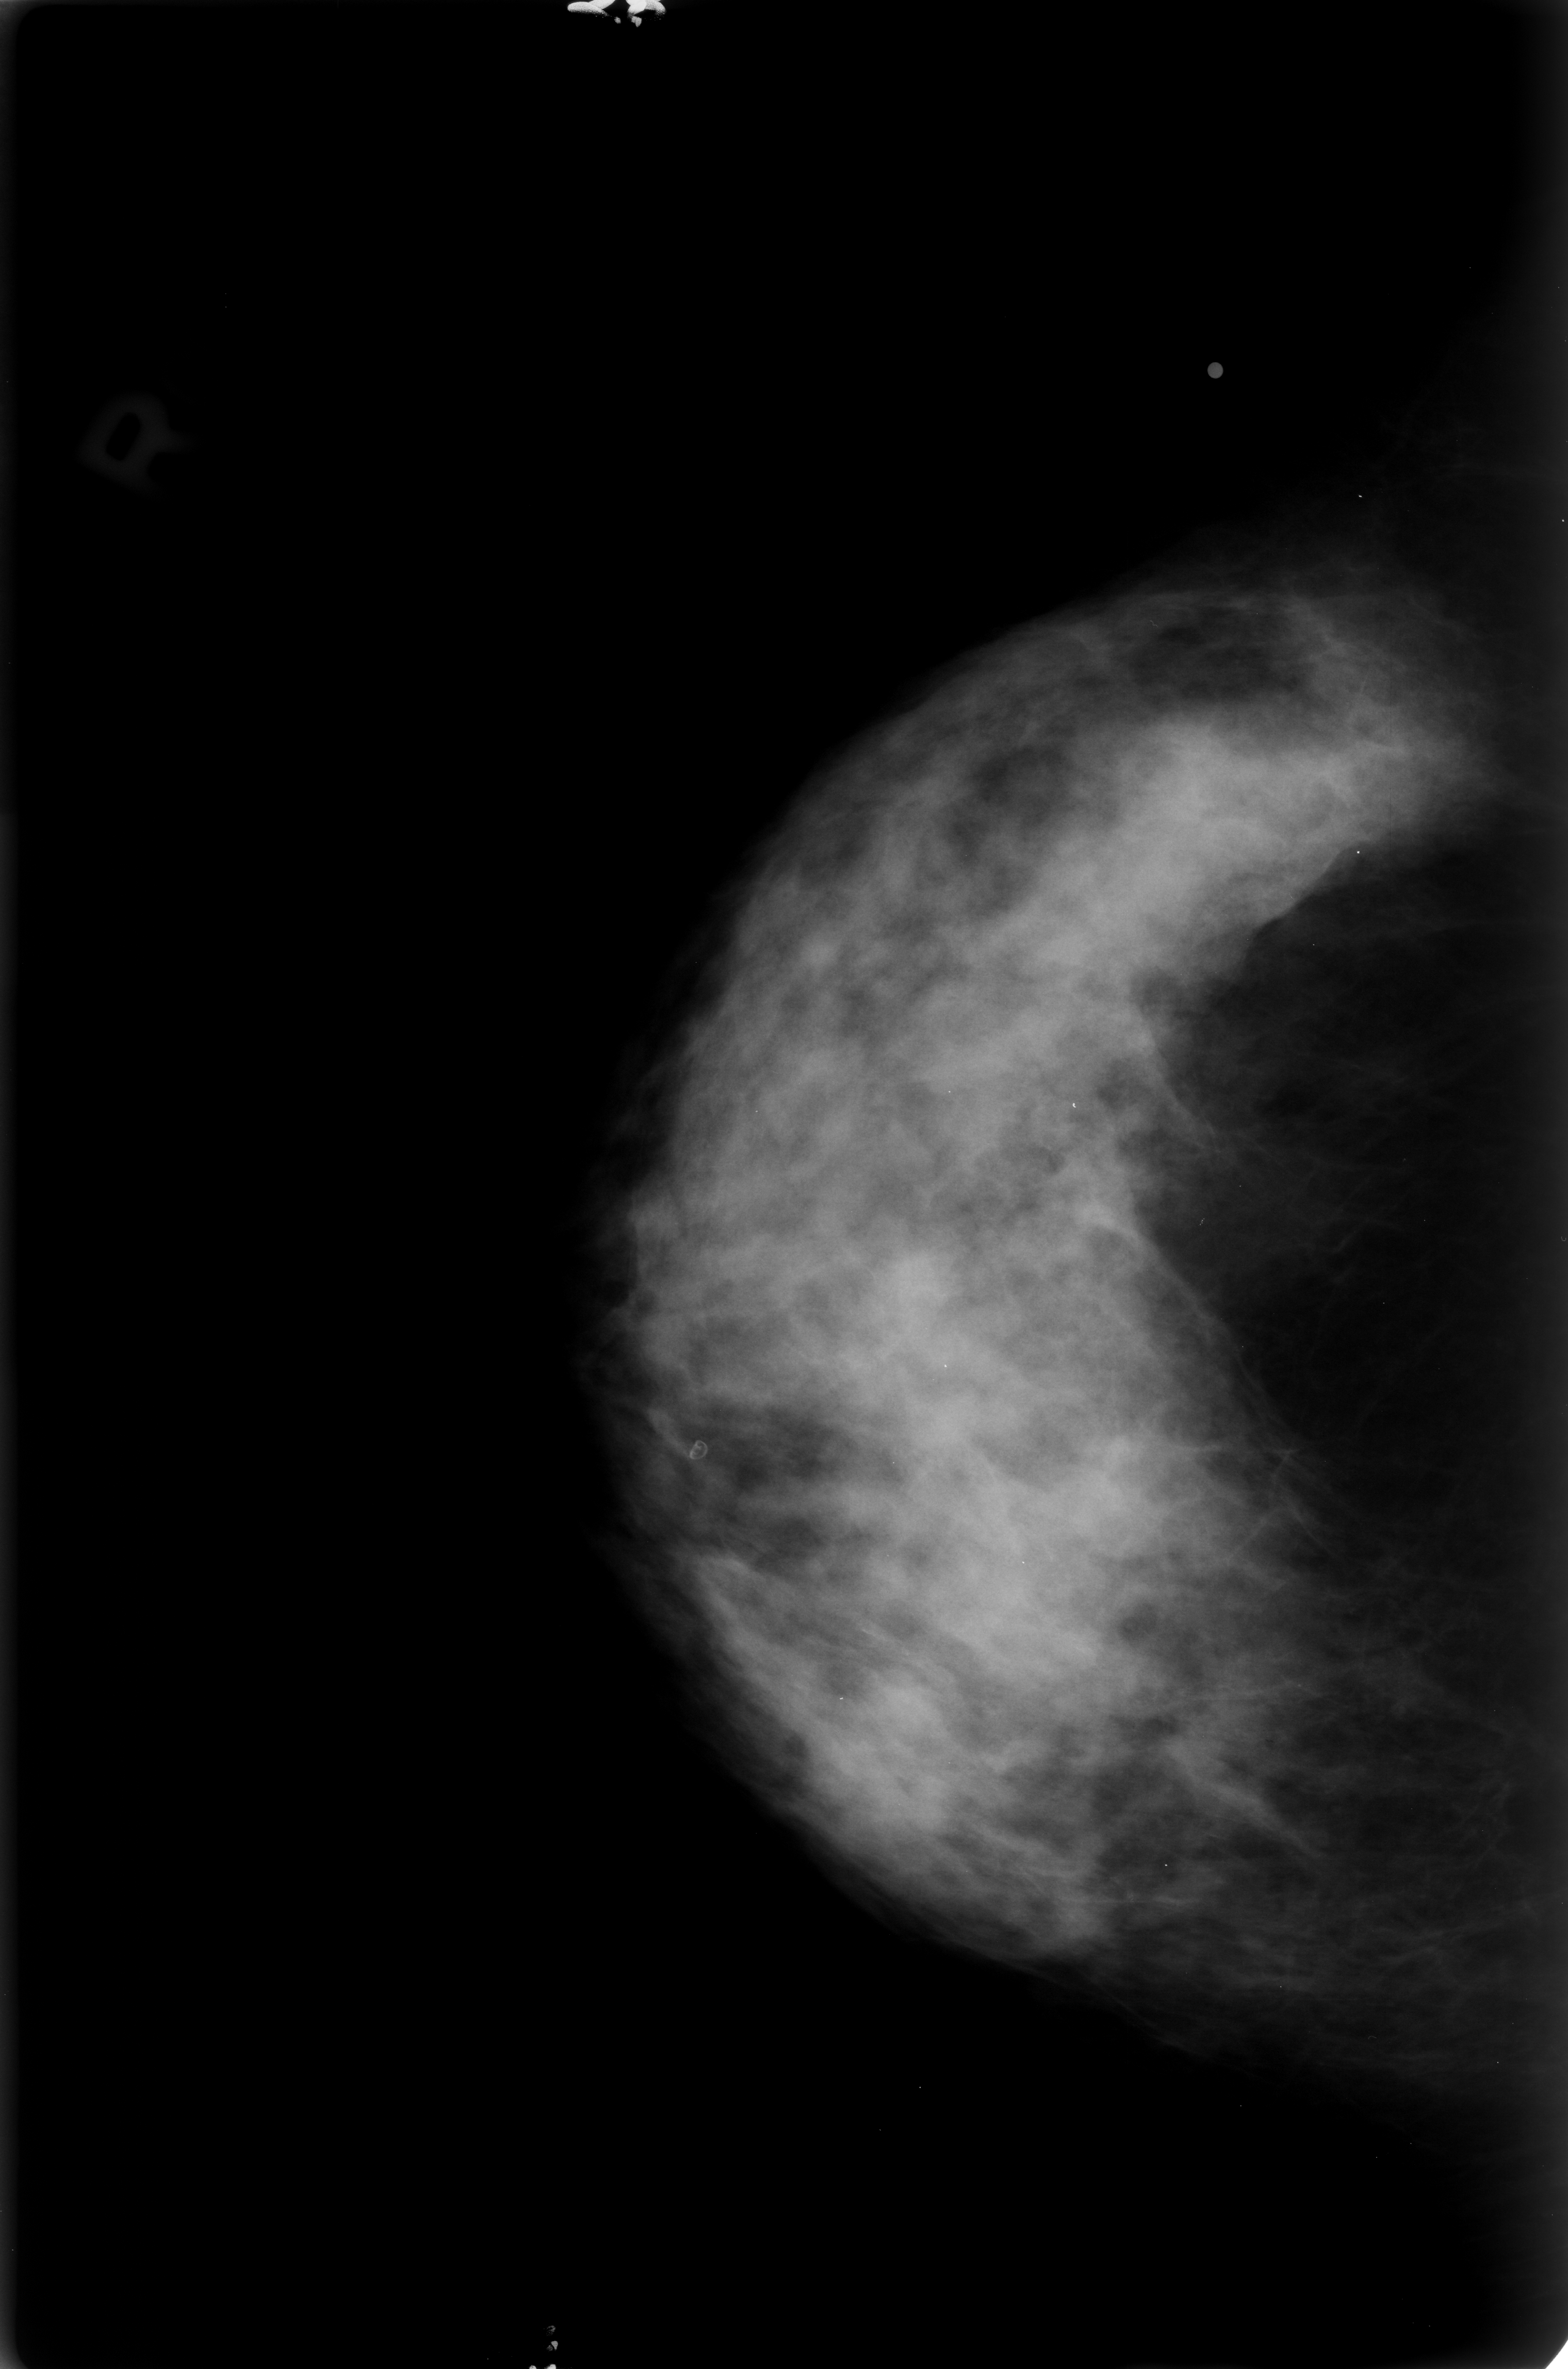
Mammogram (digitized film). Right breast. Craniocaudal (CC) view. BI-RADS breast density category 4 (scale 1–4). 1568 × 2369 image matrix.
Expert-marked regions of interest on this film, with their recorded descriptors:
- calcifications, morphology lucent center; BI-RADS assessment category 2; outcome (as recorded, no biopsy): benign without callback (not worked up further): bounding box [x1, y1, x2, y2] px = [689, 1436, 711, 1470]